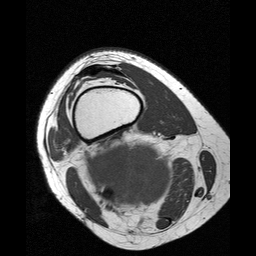
MRI of an extremity soft-tissue mass, one axial slice. Slice 22 of 25 in the series (ordered by position). 256 × 256 image matrix. Female patient. Case-level facts recorded for this patient, not image findings: histological type: liposarcoma; site of the primary tumour: right thigh.
Annotated regions visible in this slice (manually delineated by an expert):
- gross tumour volume (mass): bounding box <83,138,174,215> (left, top, right, bottom; pixels)